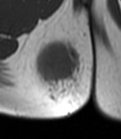
MRI of an extremity soft-tissue mass, one axial slice. Slice 16 of 47 in the series (ordered by position). MR volume resampled by the dataset authors to the PET/CT grid (not the native acquisition matrix). 121 × 139 image matrix, field of view 118 × 136 mm. Female patient. From the clinical record (not read from this slice): histological type: epithelioid sarcoma; grade: intermediate; site of the primary tumour: right buttock.
Outlined on this slice (expert contour drawn on MRI and transferred to this co-registered scan by the dataset authors):
- gross tumour volume including surrounding oedema: box from (x=34, y=36) to (x=92, y=110) px
- gross tumour volume (mass): (x=38, y=45)–(x=78, y=80)